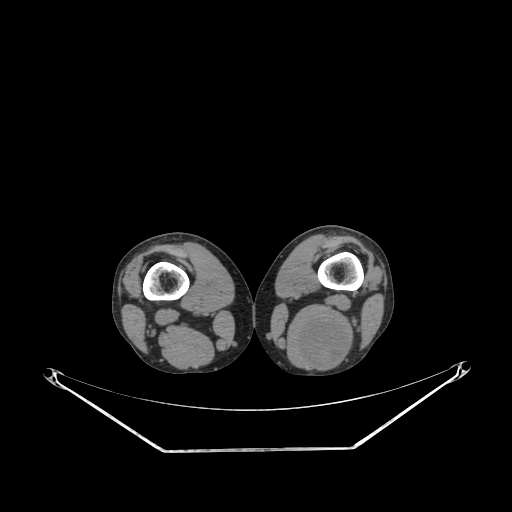
CT of an extremity soft-tissue mass (from a PET/CT study), one axial slice. Position 196 of 267 along the scan axis. Reconstruction kernel SOFT. 140 kVp. Soft-tissue window (W 400 / L 40 HU). 512 × 512 image matrix, field of view 500 × 500 mm. Male patient. Case-level facts recorded for this patient, not image findings: histological type: synovial sarcoma; site of the primary tumour: left poplietal fossa.
Structures marked on this image (expert contour drawn on MRI and transferred to this co-registered scan by the dataset authors):
- gross tumour volume (mass): bounding box [x1, y1, x2, y2] px = [295, 317, 348, 366]